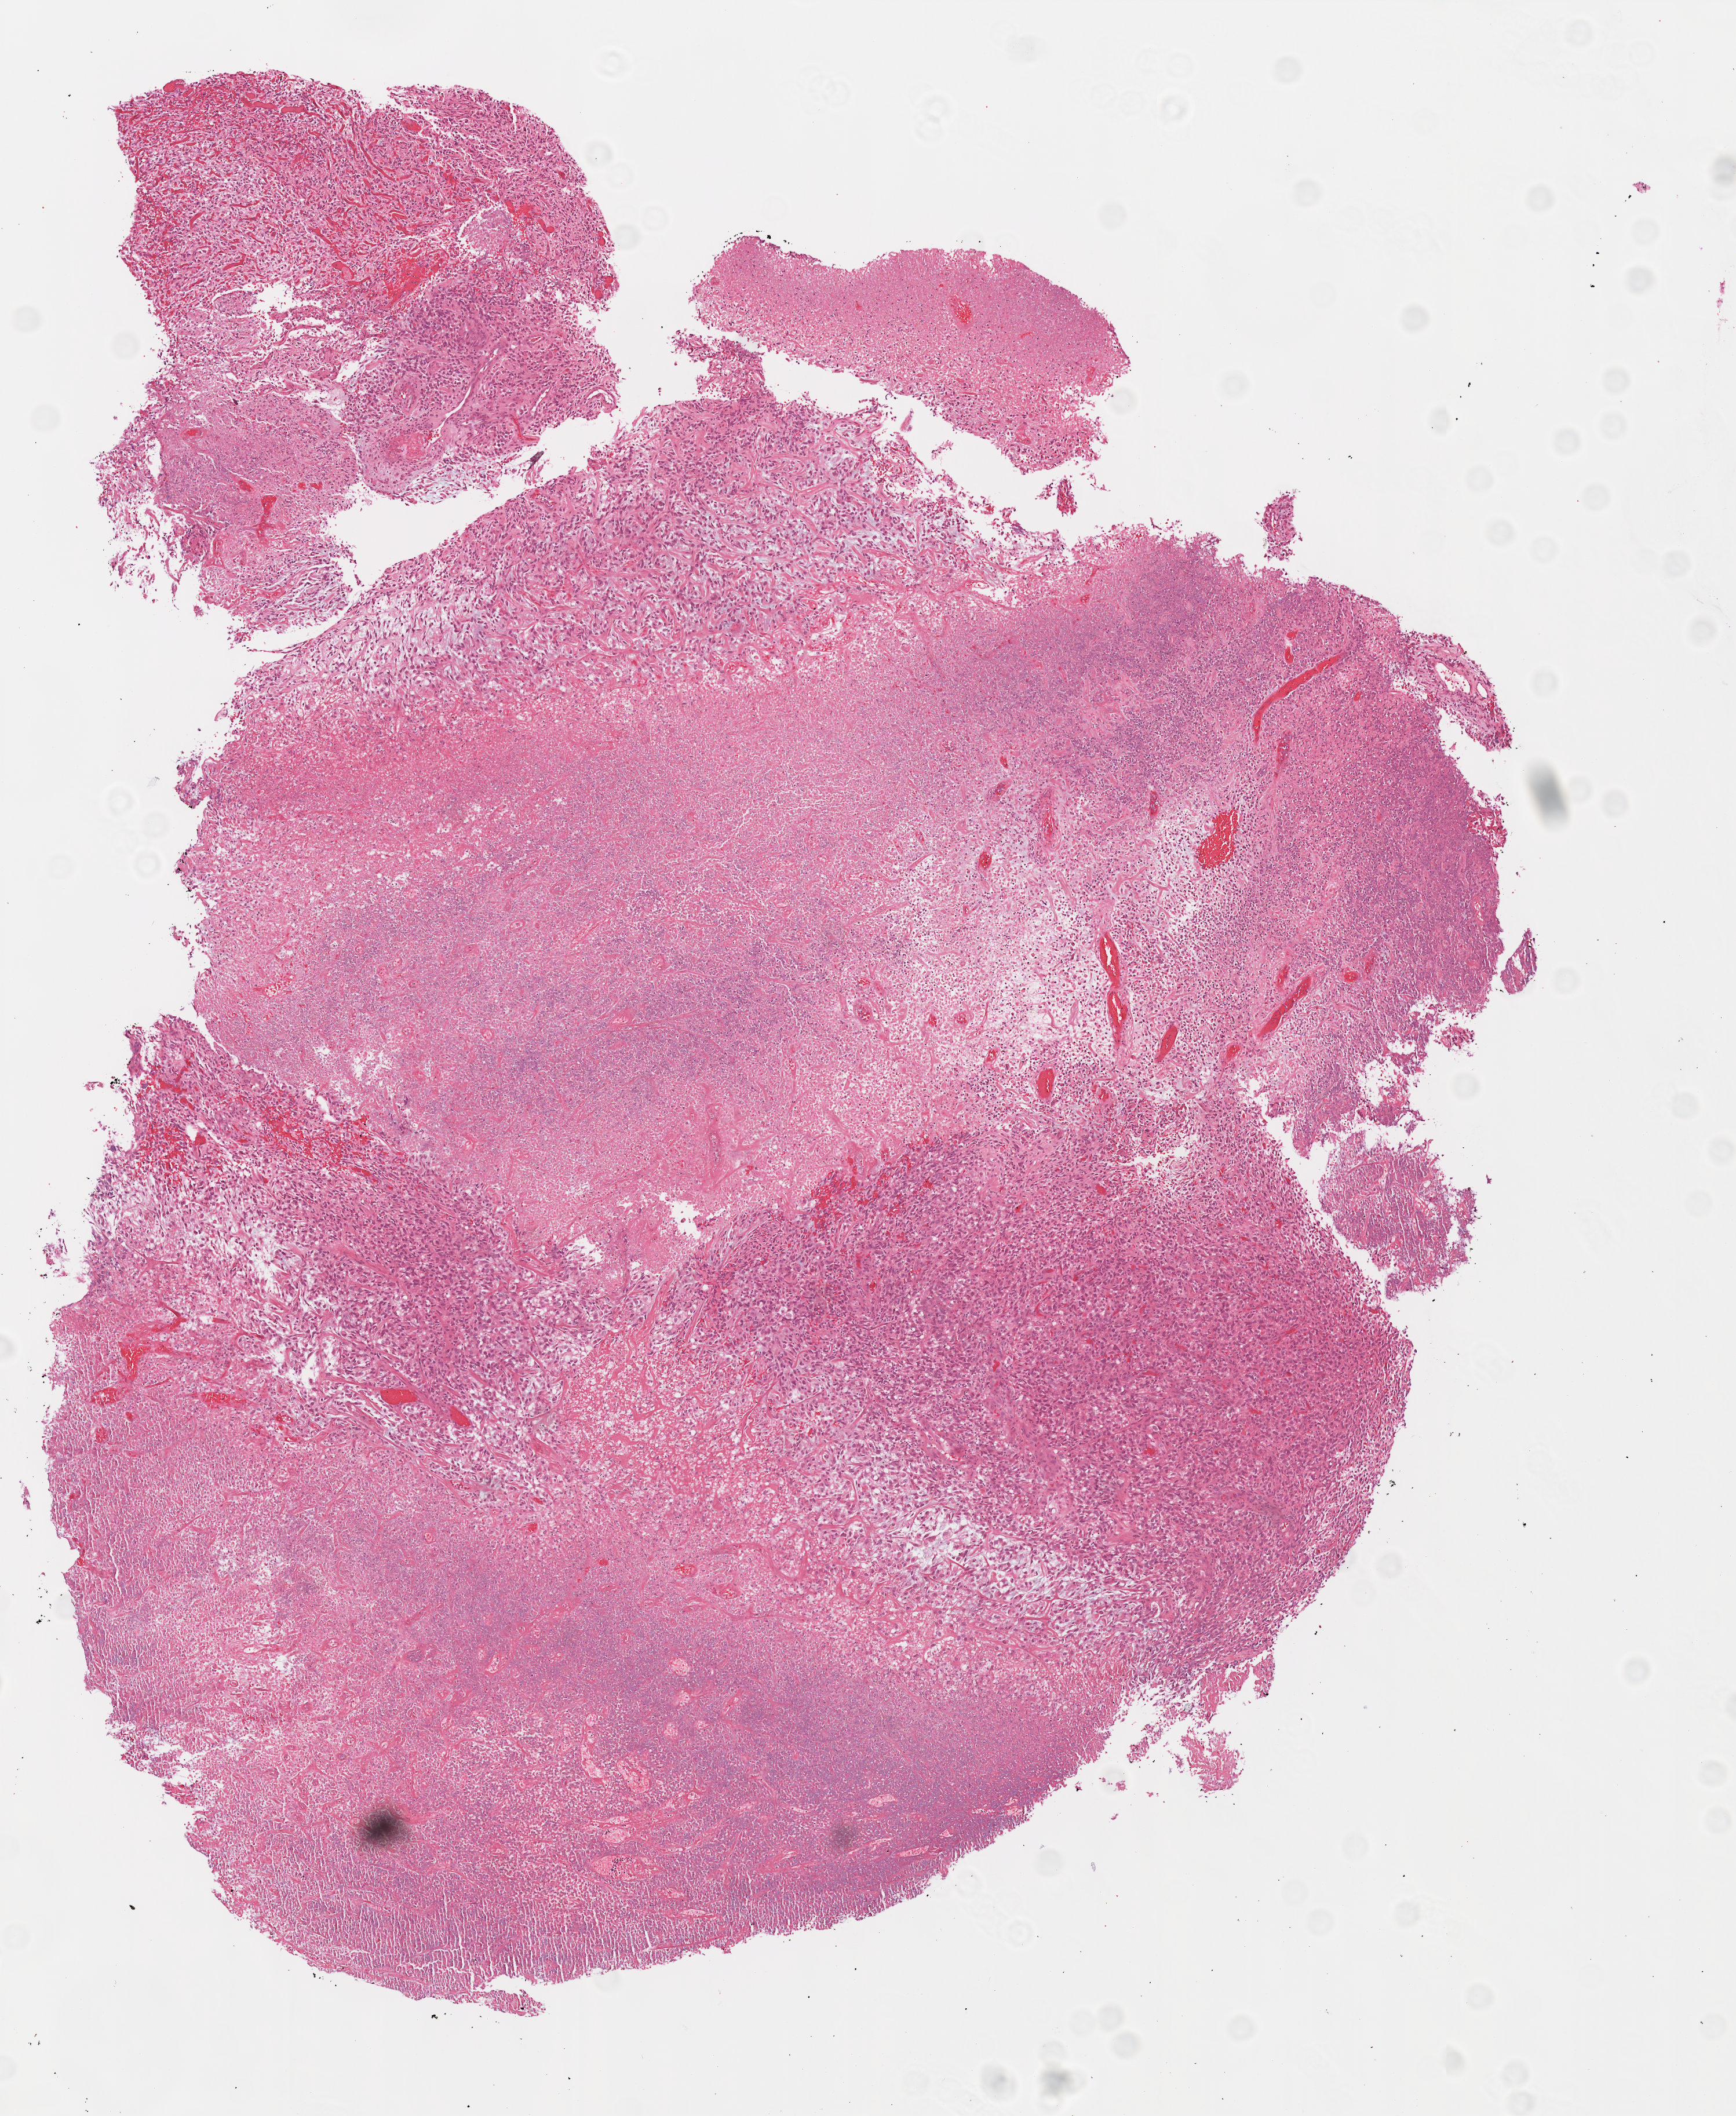
Whole-slide histology image, Hematoxylin and eosin (H&E) stained — low-resolution overview of the scanned area, about 6.0 x 7.3 mm. FFPE section. Brain, primary tumour sample. Male, age 68 years at initial diagnosis.
Pathologic diagnosis: Glioblastoma.